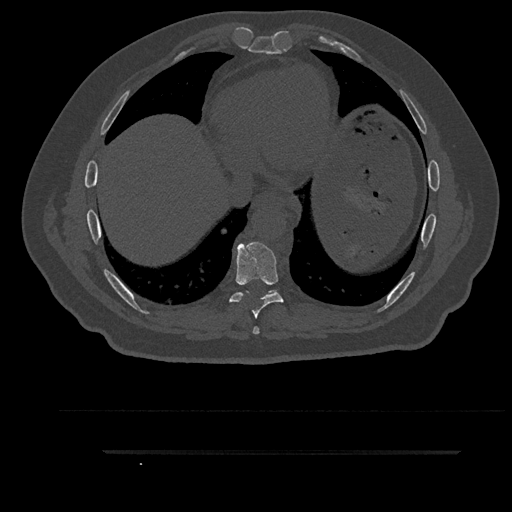
CT including the spine, one axial slice. Position 471 of 797 along the scan axis. Reconstruction kernel Br40s/3. 120 kVp. Bone window (W 1800 / L 400 HU). 0.5 mm slice thickness. 512 × 512 image matrix, field of view 432 × 432 mm. Male patient, age 63 years. From the clinical record (not read from this slice): primary cancer: renal.
Annotated regions visible in this slice (semi-automatic segmentation, software-assisted and operator-edited):
- T7 vertebra: bounding box (x1, y1, x2, y2) in pixels: (253, 326, 260, 334)
- T8 vertebra: (229, 242, 284, 318)
- T9 vertebra: (246, 291, 272, 293)